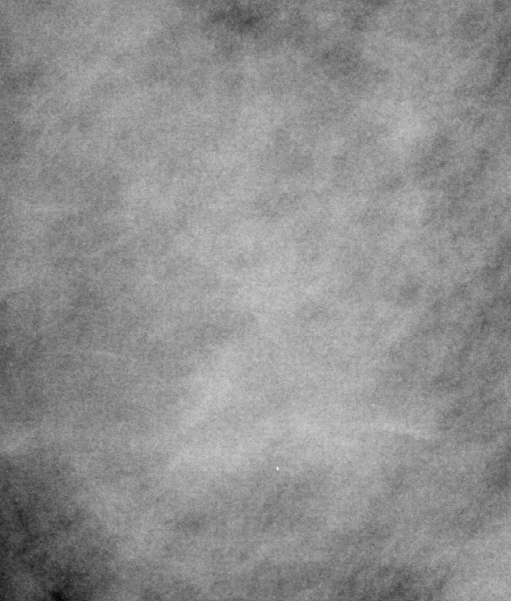
Cropped region of a digitized screen-film mammogram centred on a radiologist-marked abnormality, right breast, MLO view.
- Mass, shape oval, margins circumscribed / obscured; BI-RADS assessment category 3; pathology (as recorded): benign.